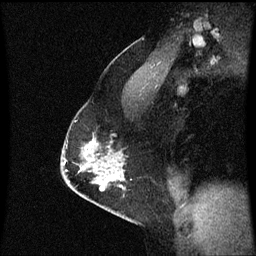
Breast MRI (dynamic contrast-enhanced), one sagittal slice. Position 41 of 60 along the scan axis. Dynamic contrast-enhanced series, image 2 of 3 at this slice position (ordered by acquisition). 1.5 T. TE 4.2 ms, TR 8.9 ms. 2 mm slice thickness. 256 × 256 image matrix. Patient: female, 47 years. From the clinical record (not read from this slice): setting: breast cancer imaged before/during neoadjuvant chemotherapy; receptor status: HR-positive, HER2-negative.
Annotated regions visible in this slice (semi-automatic segmentation, software-assisted and operator-edited):
- analysis volume of interest (the breast-tissue region the enhancement analysis was run in; not a lesion): bounding box [x1, y1, x2, y2] px = [63, 110, 128, 209]
- tumour enhancement mask (voxels above the 70 % enhancement threshold inside the analysis volume of interest): [90, 142, 94, 145]